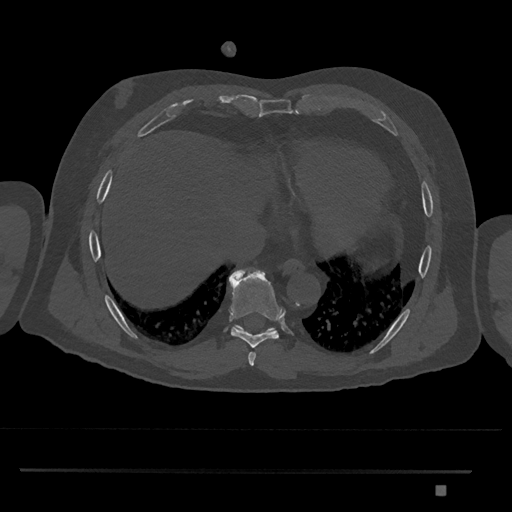
CT including the spine, one axial slice; slice 1100 of 1134 in the series (ordered by position); 120 kVp; bone window (W 1800 / L 400 HU); 0.5 mm slice thickness; 512 × 512 image matrix, field of view 429 × 429 mm. Patient: male, 65 years. From the clinical record (not read from this slice): primary cancer: prostate.
Annotated regions visible in this slice (semi-automatic segmentation, software-assisted and operator-edited):
- T8 vertebra: bounding box [x1, y1, x2, y2] px = [228, 269, 284, 347]
- T9 vertebra: [234, 324, 276, 332]